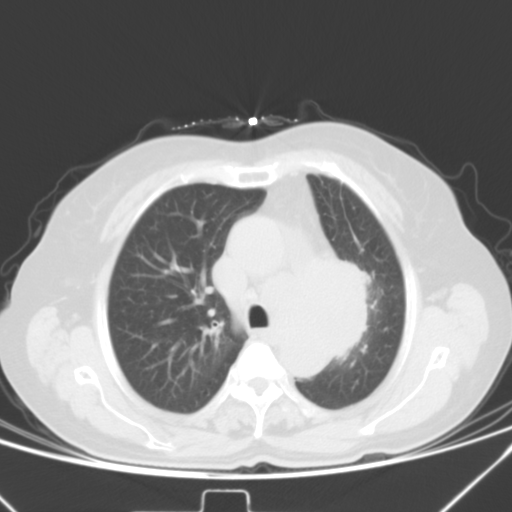
Chest CT, one axial slice; position 30 of 42 along the scan axis; lung window (W 1500 / L -600 HU); 512 × 512 image matrix, field of view 331 × 331 mm. Patient: female, 59 years. From the clinical record (not read from this slice): clinical TNM (as recorded): T3 N1 M0; histopathological grade: G3.
Annotated regions visible in this slice (bounding box drawn by a radiologist):
- lung tumour (recorded histology: small cell carcinoma): box from (x=332, y=248) to (x=390, y=372) px